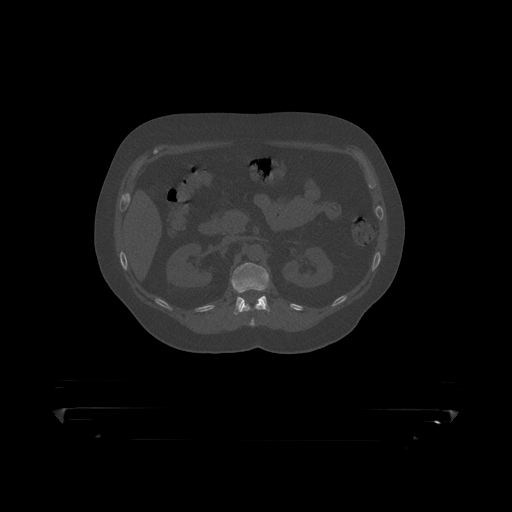
CT including the spine, one axial slice; reconstruction kernel STANDARD; bone window (W 1800 / L 400 HU); 1.25 mm slice thickness; 512 × 512 image matrix. Male patient, age 60 years. Case-level facts recorded for this patient, not image findings: primary cancer: prostate.
Annotated regions visible in this slice (semi-automatic segmentation, software-assisted and operator-edited):
- L1 vertebra: box from (x=231, y=263) to (x=270, y=315) px
- T12 vertebra: (x=238, y=300)–(x=269, y=319)